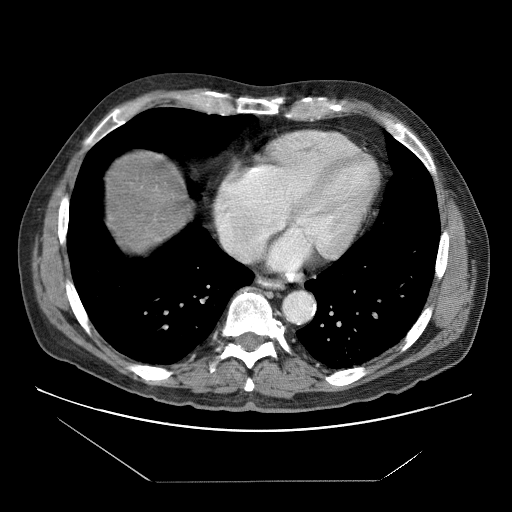
Contrast-enhanced abdominal CT (liver protocol), one axial slice; position 73 of 83 along the scan axis; reconstruction kernel STANDARD; soft-tissue window (W 400 / L 40 HU); 2.5 mm slice thickness; 512 × 512 image matrix, field of view 420 × 420 mm. From the clinical record (not read from this slice): diagnosis: hepatocellular carcinoma (patient treated with transarterial chemoembolisation; whether this scan precedes or follows treatment is not stated here); TNM stage (as recorded): Stage-IVB; Child-Pugh class: B; tumour differentiation: poorly differentiated; tumour nodularity: uninodular.
Annotated regions visible in this slice (semi-automatically segmented with operator editing):
- abdominal aorta: box from (x=285, y=293) to (x=313, y=321) px
- liver parenchyma outside the tumour (the mass and vessels are separate outlines, so this box may not span the whole liver): (x=106, y=150)–(x=190, y=252)